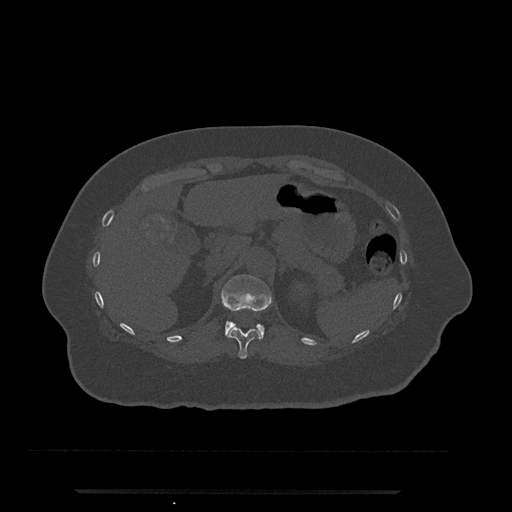
CT including the spine, one axial slice. Slice 201 of 797 in the series (ordered by position). Reconstruction kernel Br40s/3. 120 kVp. Bone window (W 1800 / L 400 HU). 0.5 mm slice thickness. 512 × 512 image matrix, field of view 440 × 440 mm. Female patient, age 51 years. From the clinical record (not read from this slice): primary cancer: neuro; vertebrae with lytic lesions (as recorded): T8.
Outlined on this slice (semi-automatic segmentation, software-assisted and operator-edited):
- T11 vertebra: bounding box (x1, y1, x2, y2) in pixels: (226, 326, 261, 359)
- T12 vertebra: (221, 275, 272, 339)